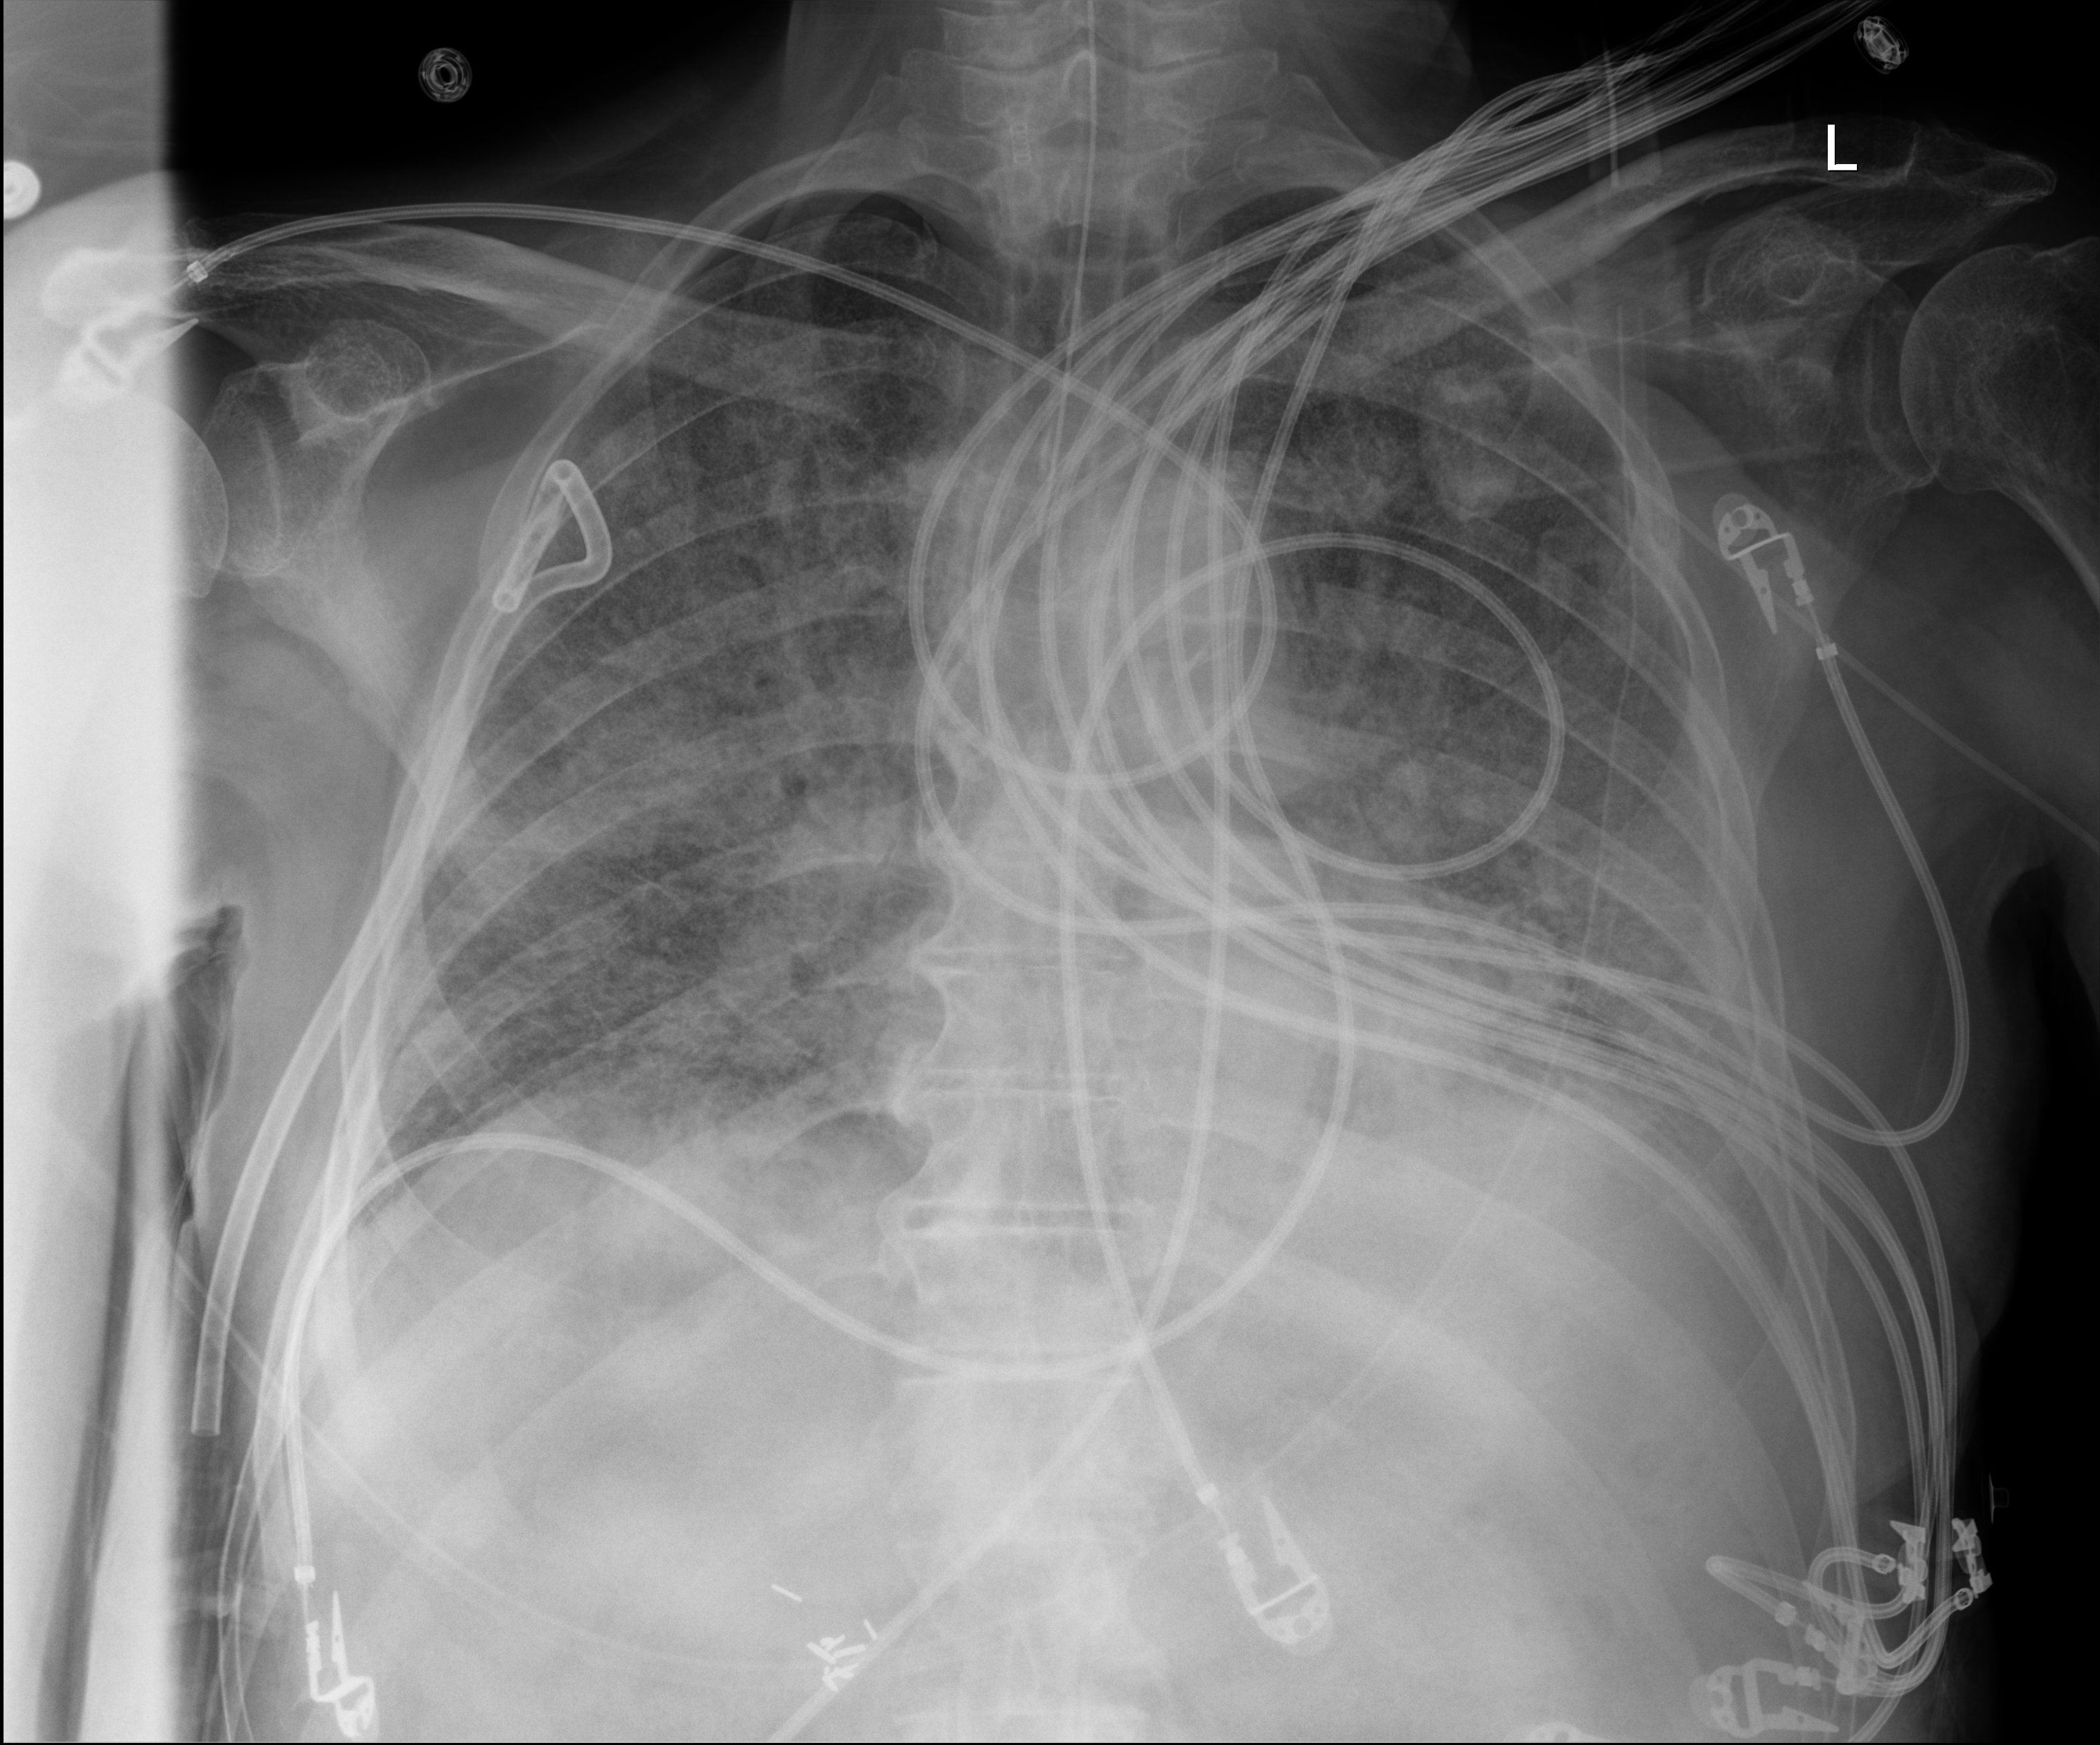
Bedside chest radiograph (digital radiography), anteroposterior (AP) projection. Male patient hospitalised with COVID-19, age 75–90 years.
Admission-level facts for this patient (not findings on this image; timing relative to this image not recorded):
- hypertension (admission record): yes
- mechanically ventilated during this hospital stay: yes